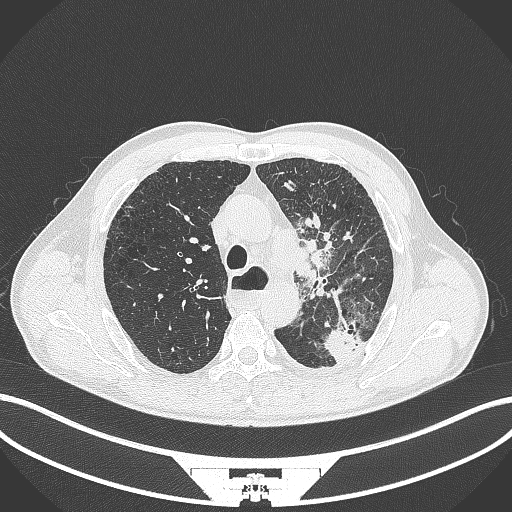
Chest CT, one axial slice. Slice 282 of 411 in the series (ordered by position). 120 kVp. Lung window (W 1500 / L -600 HU). 1 mm slice thickness. 512 × 512 image matrix, field of view 400 × 400 mm. Male patient, age 57 years. From the clinical record (not read from this slice): clinical TNM (as recorded): T2a N1 M0.
Structures marked on this image (rectangle marked by the reading radiologist):
- lung tumour (recorded histology: squamous cell carcinoma): bounding box (x1, y1, x2, y2) in pixels: (294, 236, 330, 284)